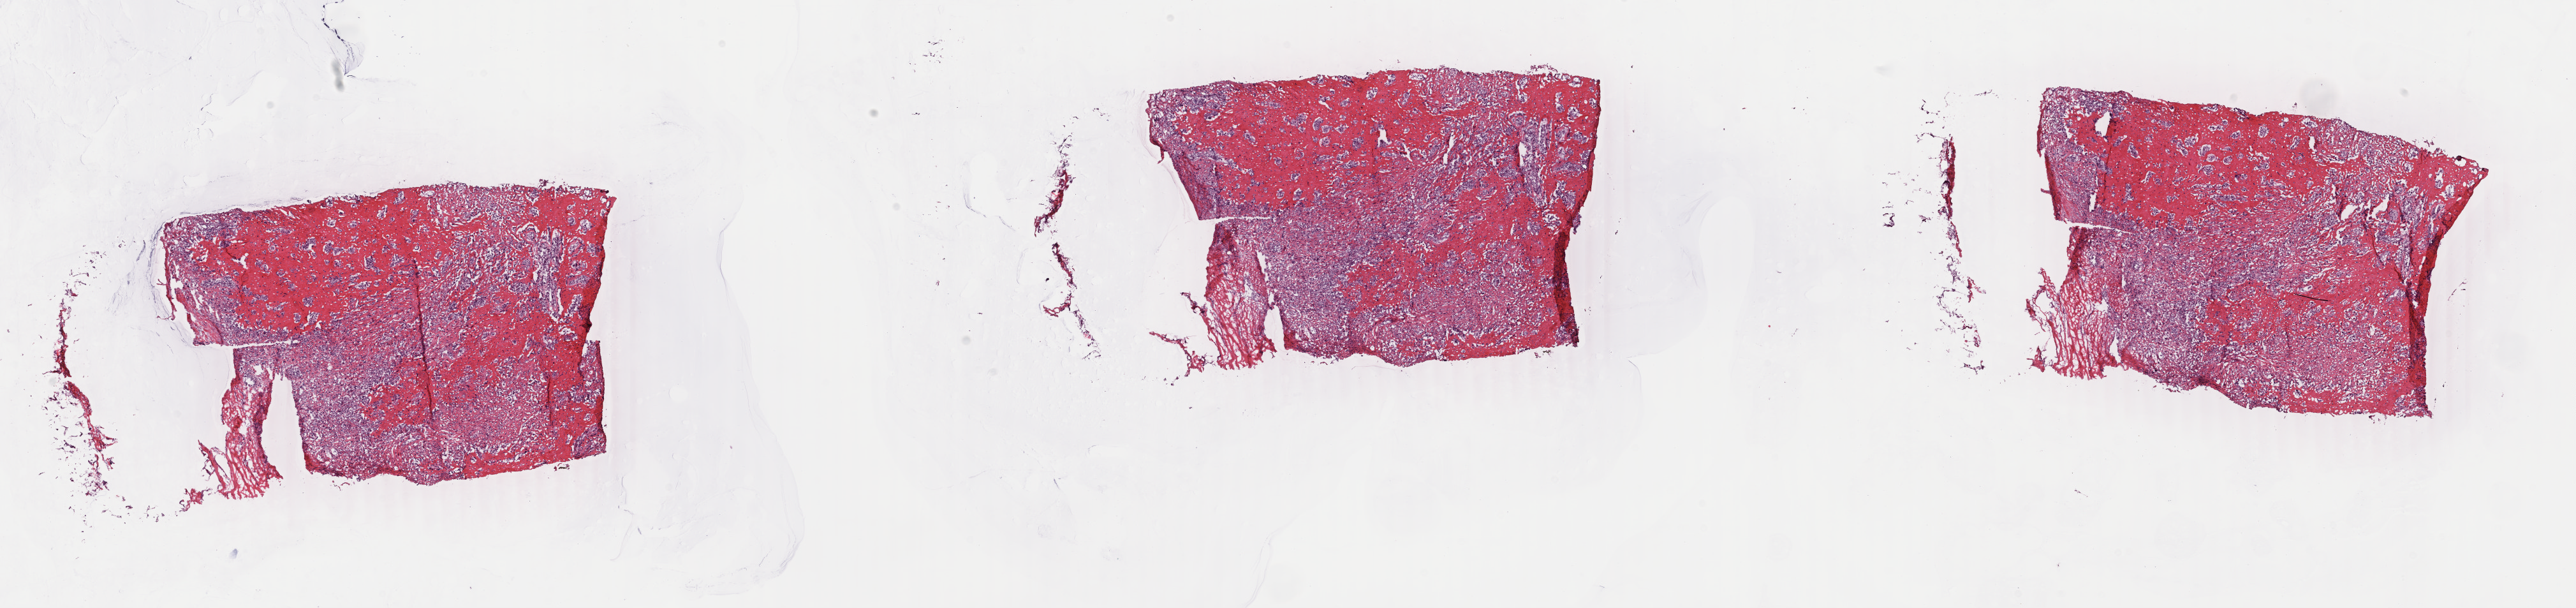
Hematoxylin and eosin (H&E) stained whole-slide image, low-resolution overview of the scanned area, about 32.1 x 7.6 mm (acquisition: 40x scan), frozen section, sample: primary tumour, breast. Patient: female, age at initial diagnosis 66 years. Pathologist review of this section (percent, as recorded): tumour cells 70%, tumour nuclei 70%, normal cells 0%, stromal cells 20%, necrosis 10%. Inflammatory infiltration, as recorded: lymphocyte infiltration 40%, monocyte infiltration 20%, neutrophil infiltration 20%.
TNM: T2 N0 M0. AJCC pathologic stage: IIA (7th edition). Histologic diagnosis: Metaplastic carcinoma, NOS. Laterality: right.